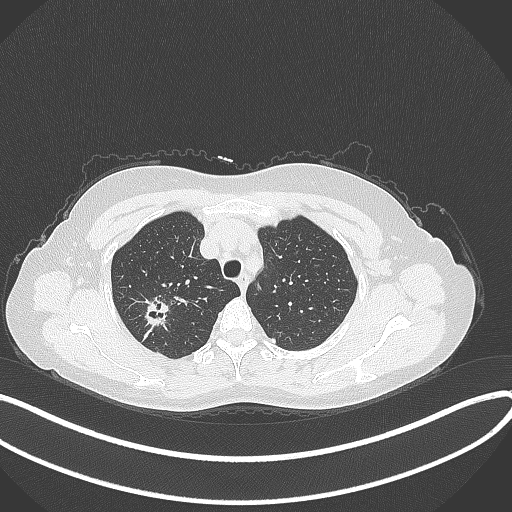
Chest CT, one axial slice; position 293 of 337 along the scan axis; reconstruction kernel B70f; 120 kVp; lung window (W 1500 / L -600 HU); 512 × 512 image matrix, field of view 400 × 400 mm. Patient: female, 50 years. From the clinical record (not read from this slice): clinical TNM (as recorded): T1c N0 M0; histopathological grade: G2-3.
Annotated regions visible in this slice (rectangle marked by the reading radiologist):
- lung tumour (recorded histology: adenocarcinoma): bounding box (x1, y1, x2, y2) in pixels: (140, 293, 176, 329)